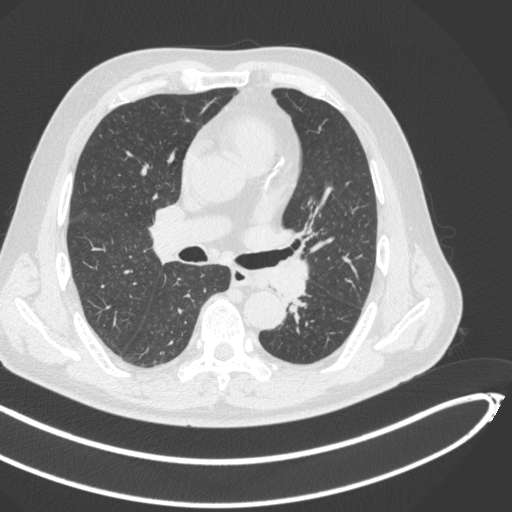
Chest CT, one axial slice; slice 264 of 466 in the series (ordered by position); lung window (W 1500 / L -600 HU); 1 mm slice thickness; 512 × 512 image matrix, field of view 400 × 400 mm. Male patient, age 64 years. From the clinical record (not read from this slice): clinical TNM (as recorded): T1c N0 M0; histopathological grade: G2.
Annotated regions visible in this slice (bounding box drawn by a radiologist):
- lung tumour (recorded histology: squamous cell carcinoma): box from (x=251, y=256) to (x=309, y=304) px